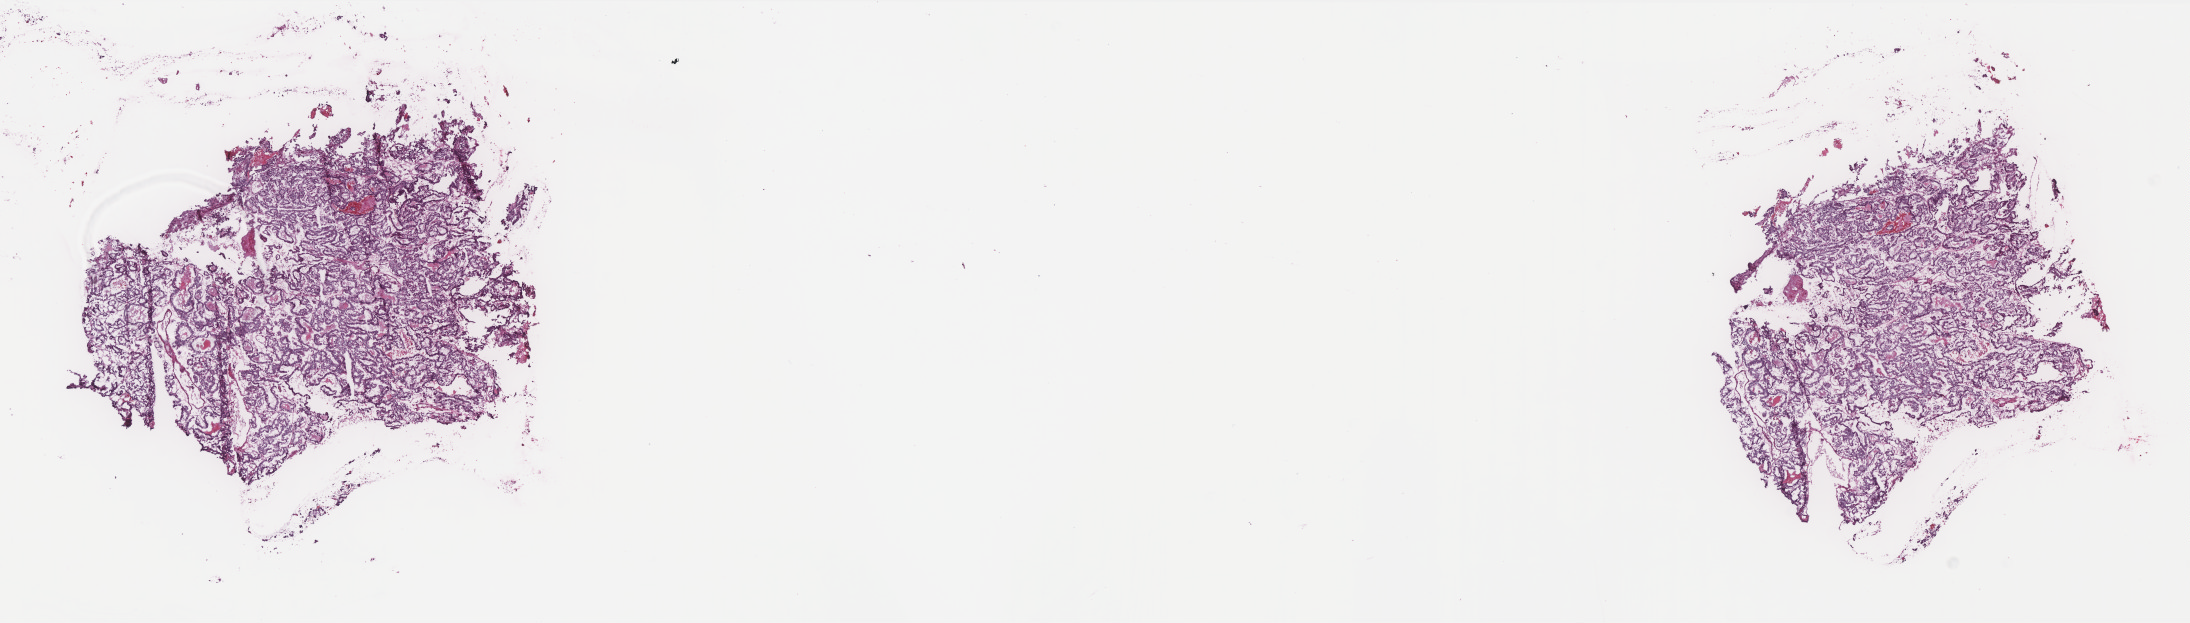
Digitized Hematoxylin and eosin (H&E) stained tissue section (whole slide) — a low-resolution overview of the entire scanned area, about 17.6 x 5.0 mm (from a 40x scan), frozen section from the top of the tissue portion, primary tumour sample from the thyroid. Female patient; age at initial diagnosis 32 years. Composition of this section per pathologist review: tumour cells 100%, tumour nuclei 93%, normal cells 0%, stromal cells 0%, necrosis 0%. Inflammatory infiltration, as recorded: lymphocyte infiltration 0%, monocyte infiltration 0%, neutrophil infiltration 0%.
• diagnosis: Papillary adenocarcinoma, NOS (thyroid gland)
• AJCC pathologic stage: I
• lymph nodes positive (case pathology): 0 of 3 examined